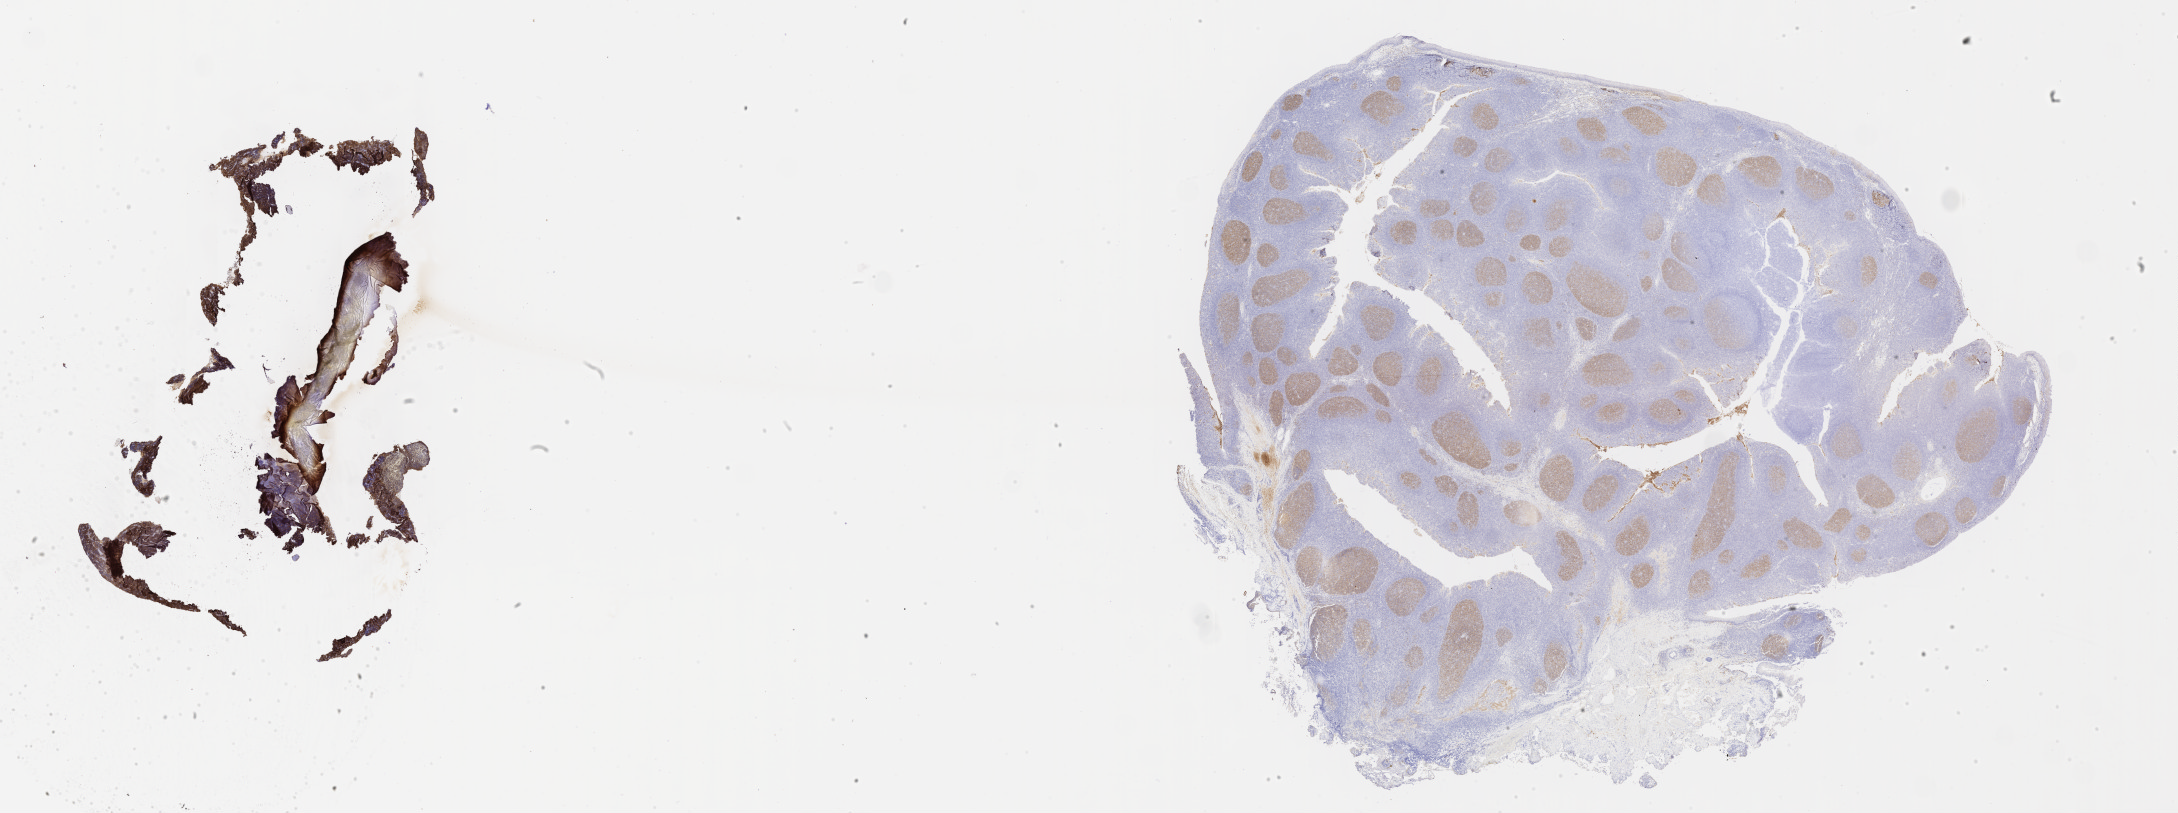
IHC for CD10, whole-slide image, a low-resolution overview of the entire scanned area, about 35.2 x 13.1 mm, specimen: tumor tissue, anatomic site: cranium. Patient: female, aged 10.
Histologic diagnosis: Burkitt lymphoma, NOS.